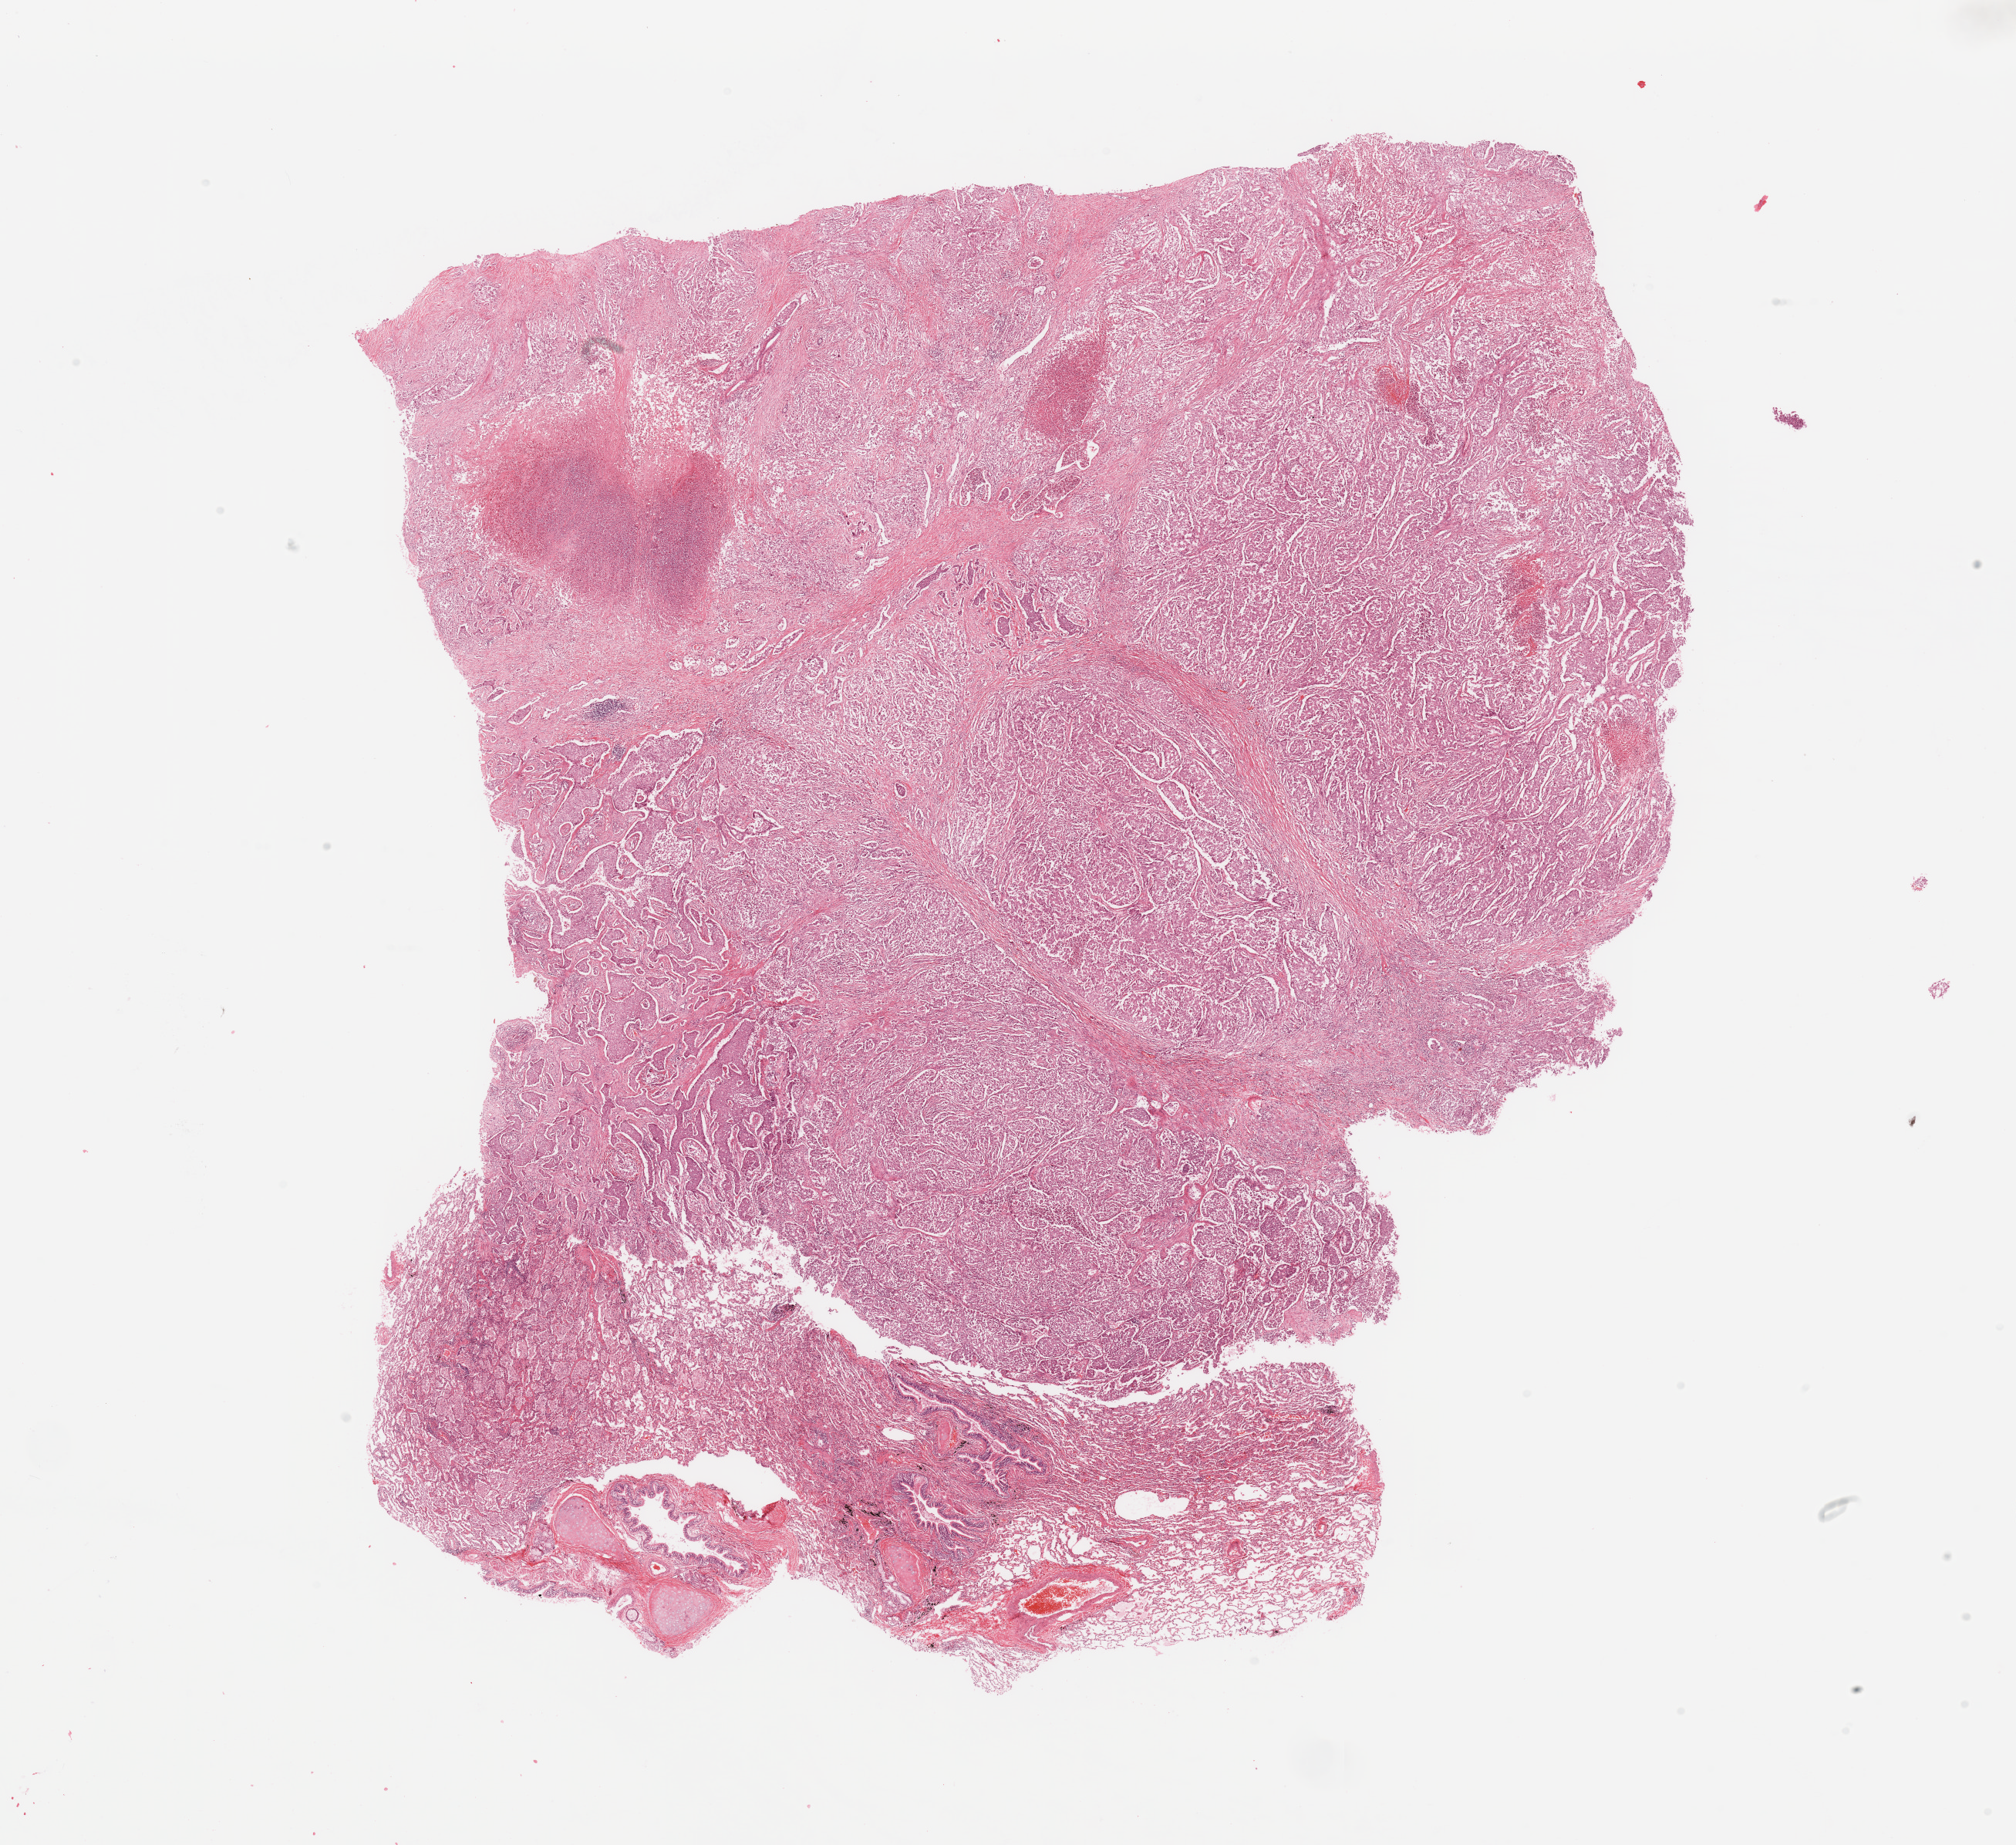
Digitized Hematoxylin and eosin (H&E) stained tissue section (whole slide) — shown as a low-resolution overview of the whole scanned area (about 20.7 x 18.9 mm); tumour tissue sample, sampled site: lung. Patient: female, age 49 years. Histologic grade: G3 (poorly differentiated). Slide review estimates, as recorded: tumour nuclei 80%, necrosis 10%.
AJCC pathologic stage: IB. Diagnosis: Adenocarcinoma, NOS.